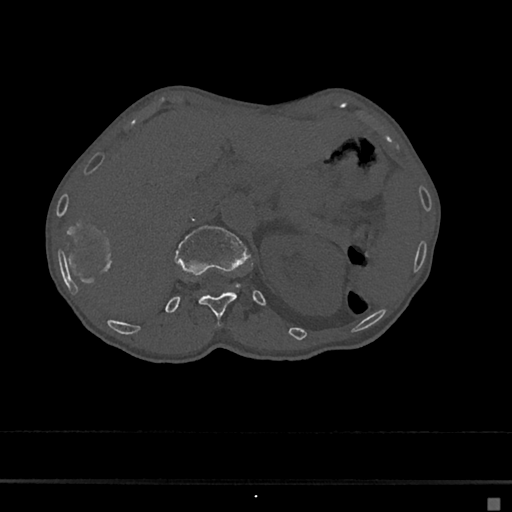
CT including the spine, one axial slice; slice 108 of 797 in the series (ordered by position); 120 kVp; bone window (W 1800 / L 400 HU); 512 × 512 image matrix. Female patient, age 68 years. Case-level facts recorded for this patient, not image findings: primary cancer: renal.
Annotated regions visible in this slice (semi-automatically segmented with operator editing):
- L1 vertebra: bounding box <174,226,248,273> (left, top, right, bottom; pixels)
- T12 vertebra: <198,292,237,318>